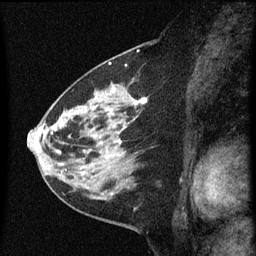
Breast MRI (dynamic contrast-enhanced), one sagittal slice; slice 29 of 60 in the series (ordered by position); dynamic contrast-enhanced series, image 2 of 3 at this slice position (ordered by acquisition); 1.5 T; TE 4.2 ms, TR 8 ms; 2 mm slice thickness; 256 × 256 image matrix. Female patient, age 60 years.
Outlined on this slice (semi-automatically segmented with operator editing):
- analysis volume of interest (the breast-tissue region the enhancement analysis was run in; not a lesion): box from (x=48, y=82) to (x=149, y=183) px
- tumour enhancement mask (voxels above the 70 % enhancement threshold inside the analysis volume of interest): (x=52, y=90)–(x=148, y=175)